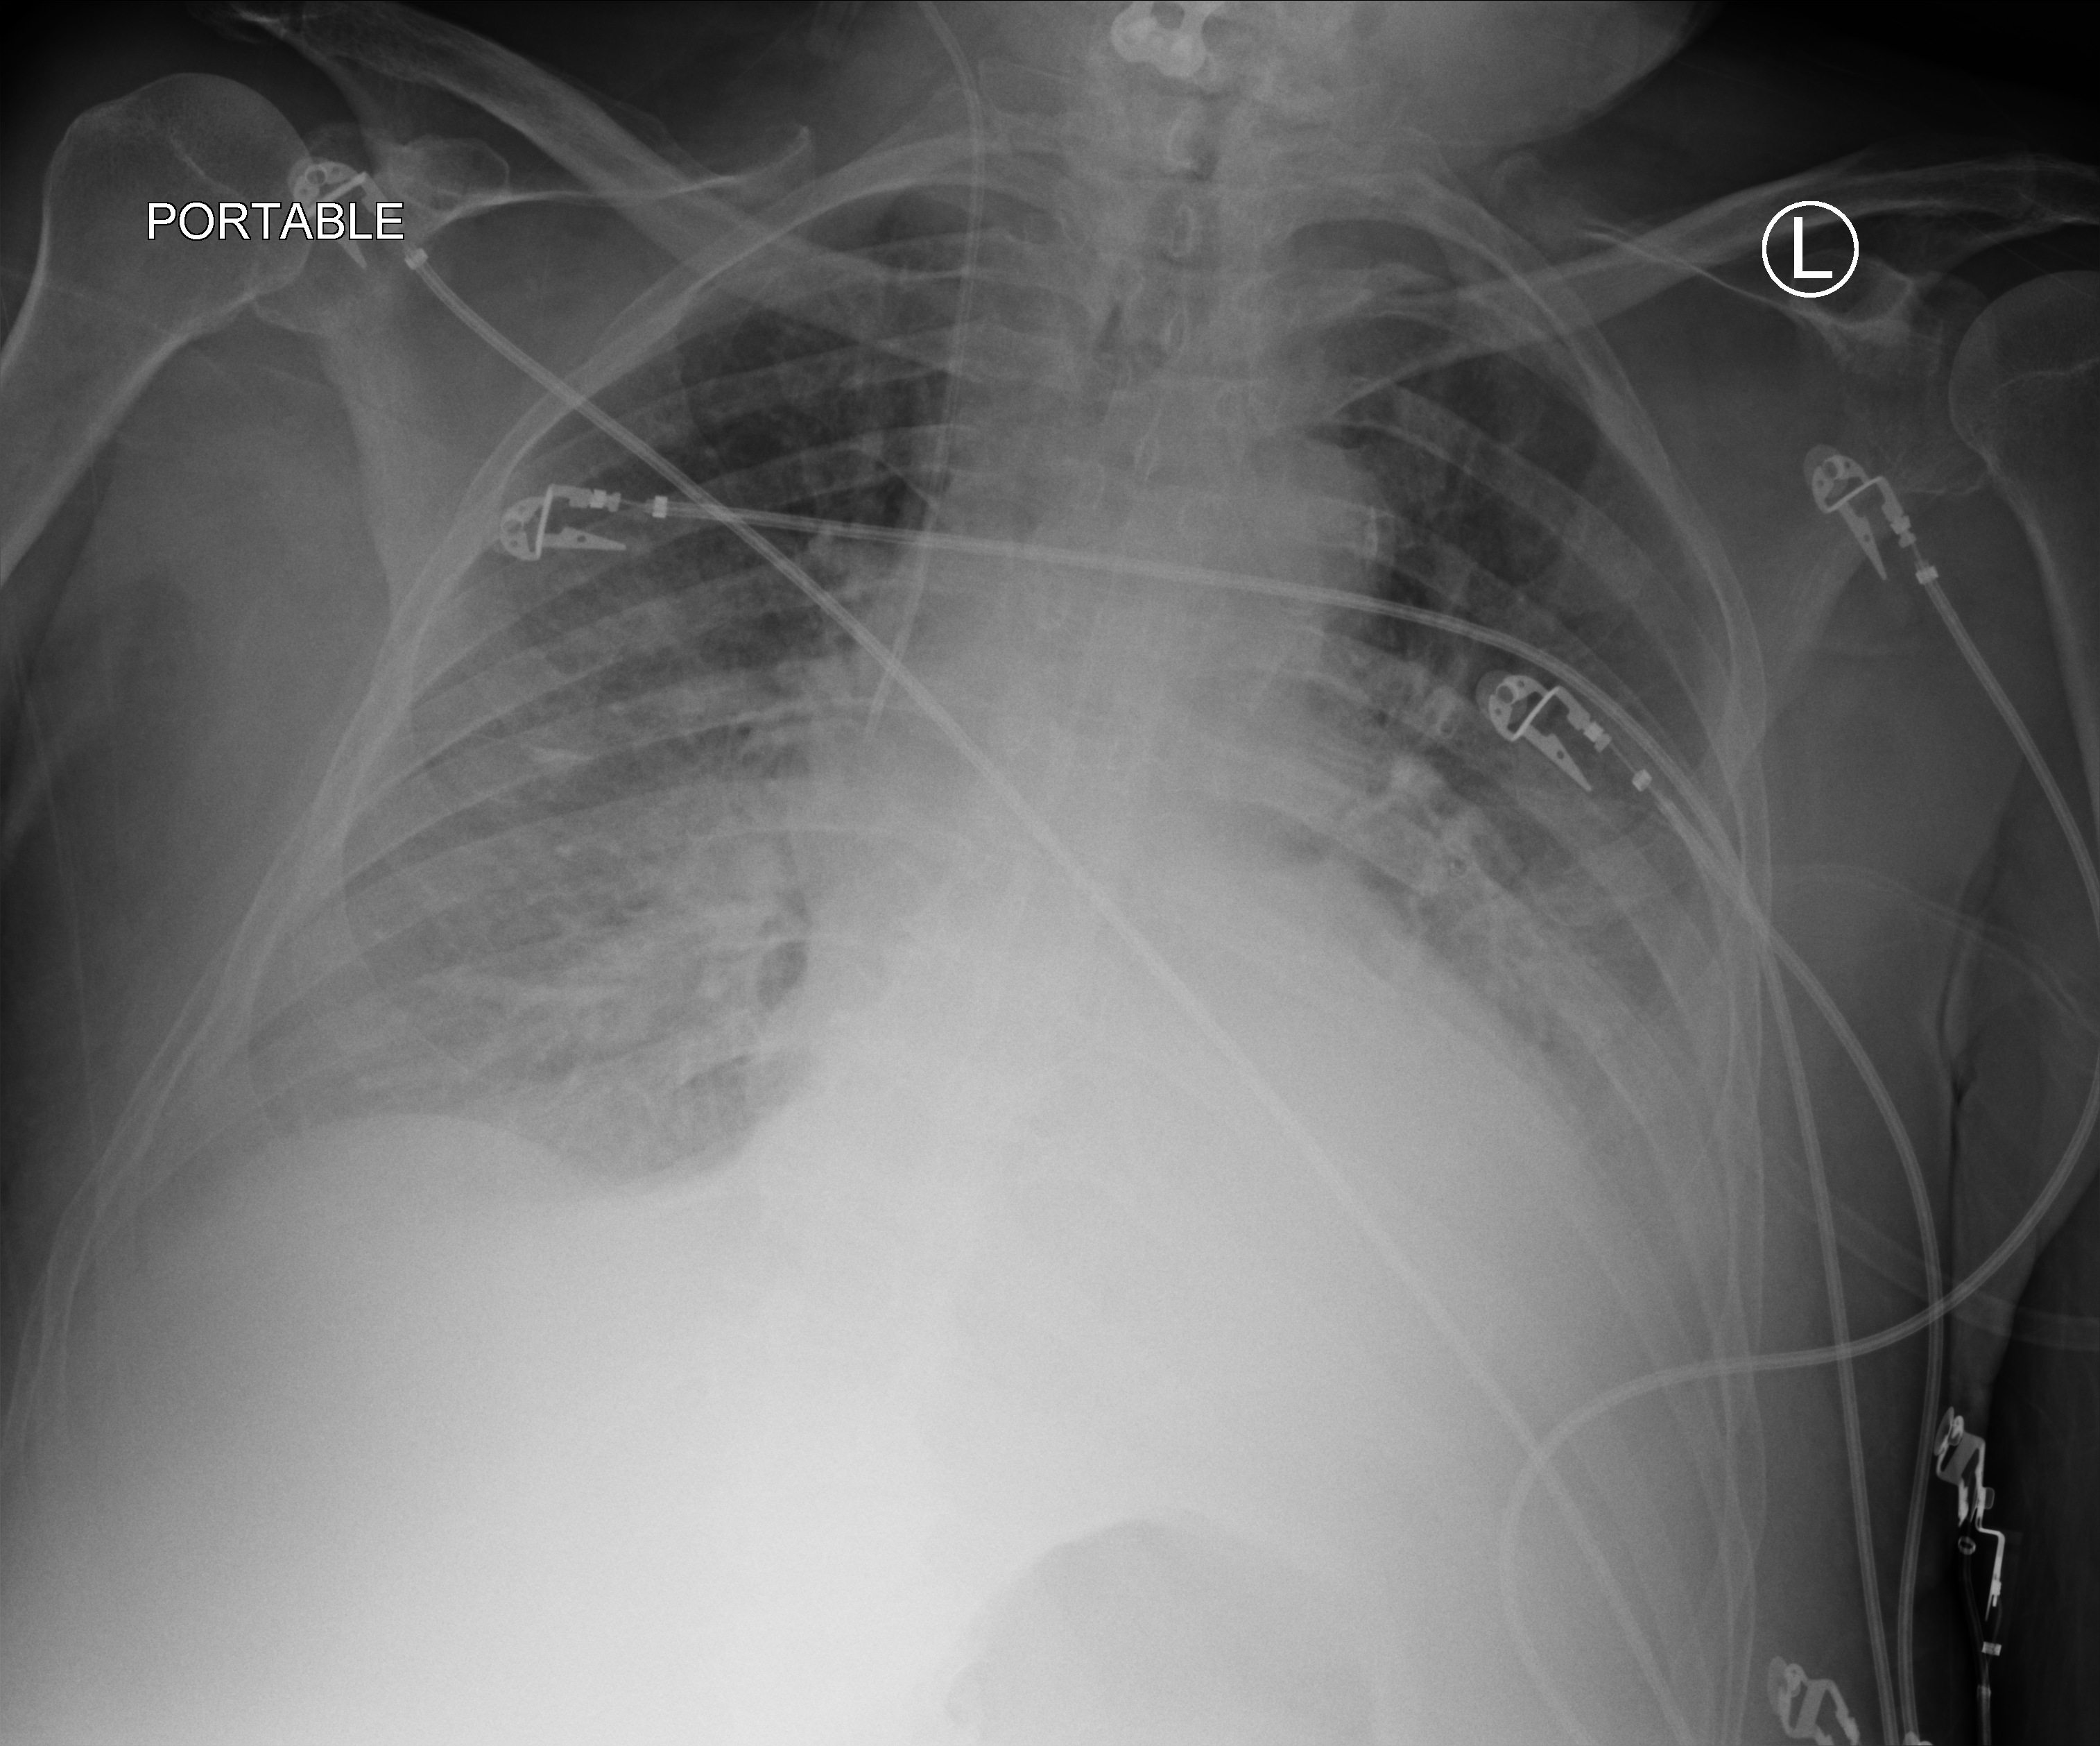
Chest X-ray (portable). Male patient hospitalised with COVID-19, age 75–90 years.
Admission-level facts for this patient (not findings on this image; timing relative to this image not recorded): chronic kidney disease (admission record): no; mechanically ventilated during this hospital stay: no; admitted to intensive care during this hospital stay: yes.